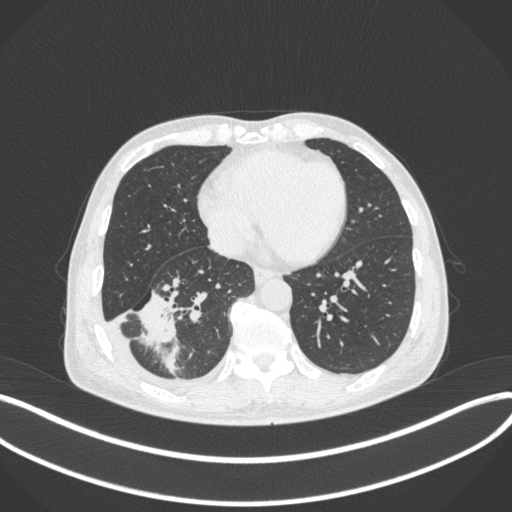
Chest CT, one axial slice. Position 134 of 385 along the scan axis. Reconstruction kernel B31f. Lung window (W 1500 / L -600 HU). 512 × 512 image matrix, field of view 400 × 400 mm. Male patient, age 64 years. From the clinical record (not read from this slice): clinical TNM (as recorded): T3 N0 M0.
Annotated regions visible in this slice (bounding box drawn by a radiologist):
- lung tumour (recorded histology: adenocarcinoma): bounding box <130,283,183,346> (left, top, right, bottom; pixels)